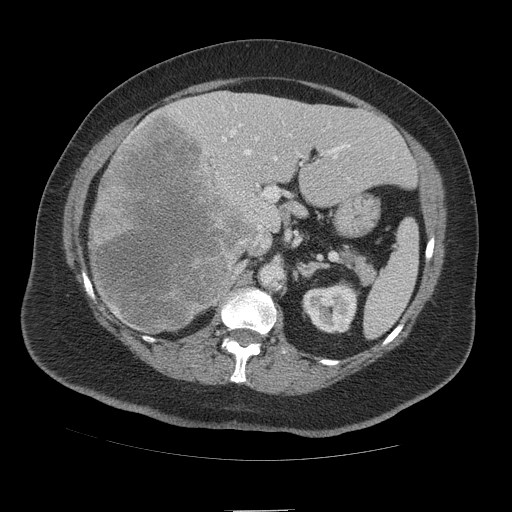
Contrast-enhanced abdominal CT (liver protocol), one axial slice. Position 59 of 109 along the scan axis. 140 kVp. Soft-tissue window (W 400 / L 40 HU). 2.5 mm slice thickness. 512 × 512 image matrix, field of view 420 × 420 mm. From the clinical record (not read from this slice): diagnosis: hepatocellular carcinoma (patient treated with transarterial chemoembolisation; whether this scan precedes or follows treatment is not stated here); TNM stage (as recorded): Stage-IVB; Child-Pugh class: A.
Annotated regions visible in this slice (semi-automatic segmentation, software-assisted and operator-edited):
- liver parenchyma outside the tumour (the mass and vessels are separate outlines, so this box may not span the whole liver): bounding box <92,90,416,331> (left, top, right, bottom; pixels)
- mass: <89,111,252,334>
- liver vessels: <192,105,349,247>